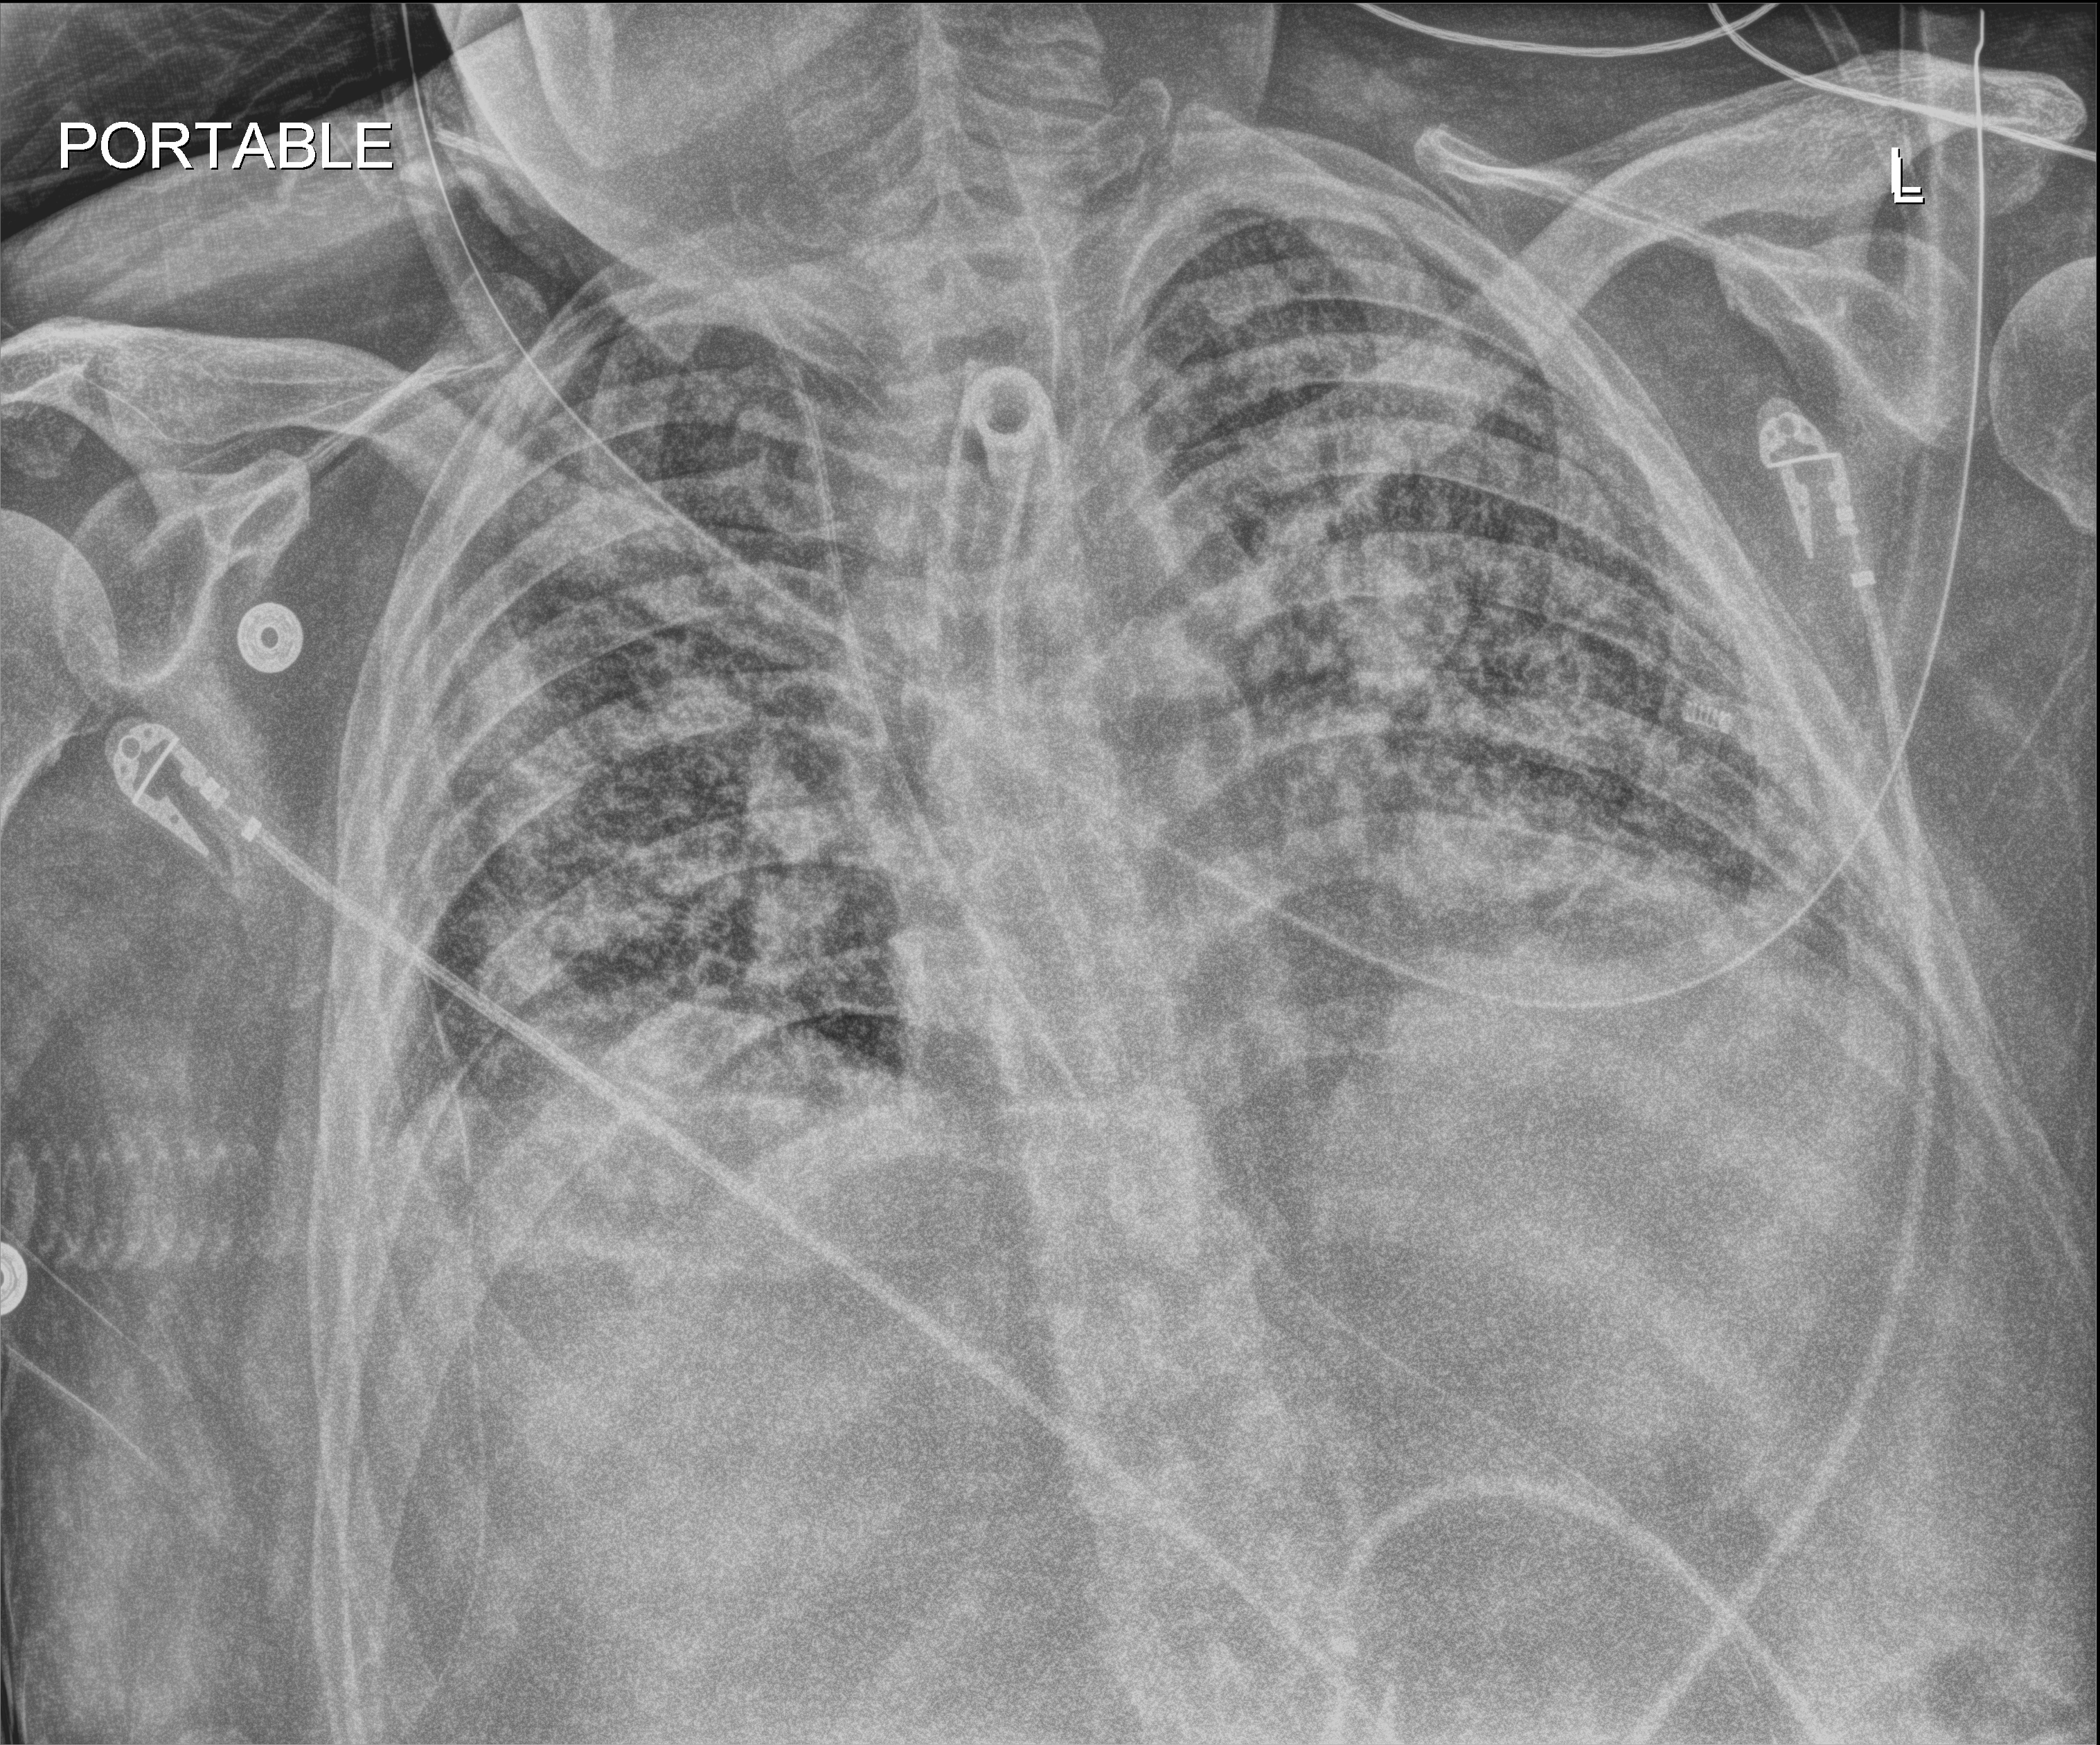
Bedside chest radiograph (digital radiography). Male patient hospitalised with COVID-19, age 18–59 years.
Hospital-stay facts (about this admission, not read from this image; timing relative to this image not recorded): smoking status (admission record): never; COPD (admission record): no; mechanically ventilated during this hospital stay: yes.